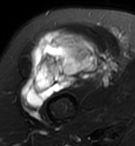
MRI of an extremity soft-tissue mass, one axial slice. Slice 71 of 95 in the series (ordered by position). T2-weighted fat-saturated. MR volume resampled by the dataset authors to the PET/CT grid (not the native acquisition matrix). 3.27 mm slice thickness. 135 × 146 image matrix. Female patient. From the clinical record (not read from this slice): histological type: pleiomorphic undifferentiated sarcoma; grade: high; site of the primary tumour: right quadricep.
Annotated regions visible in this slice (expert contour drawn on MRI and transferred to this co-registered scan by the dataset authors):
- gross tumour volume including surrounding oedema: bounding box [x1, y1, x2, y2] px = [21, 29, 100, 106]
- gross tumour volume (mass): [21, 29, 100, 106]